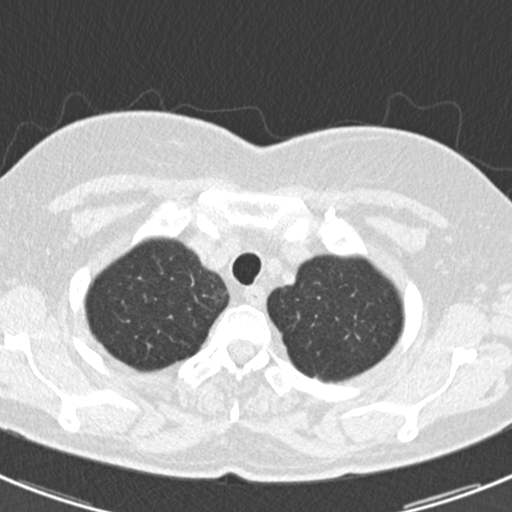
Axial slice from a low-dose chest CT screening exam, first (baseline) screen, lung window (W 1500 / L -600 HU), 2 mm slice thickness, standard (soft-tissue) reconstruction kernel (B30f), 120 kVp, 512 × 512 image matrix, field of view 298 × 298 mm. Female, age 60 years at enrolment.
- Expert reader's lesion annotation, bounding box (x1, y1, x2, y2) in pixels: (336, 310, 395, 368).
- The screening reader recorded 3 non-calcified nodules or masses ≥4 mm on this exam (lingula, left lower lobe, lingula); which of them this box marks is not recorded.
- Lung cancer was diagnosed 886 days after this screen (after the third annual screen): non-small cell carcinoma, left upper lobe, poorly differentiated (G3), stage IB (AJCC 6th edition), 7 mm at pathology.